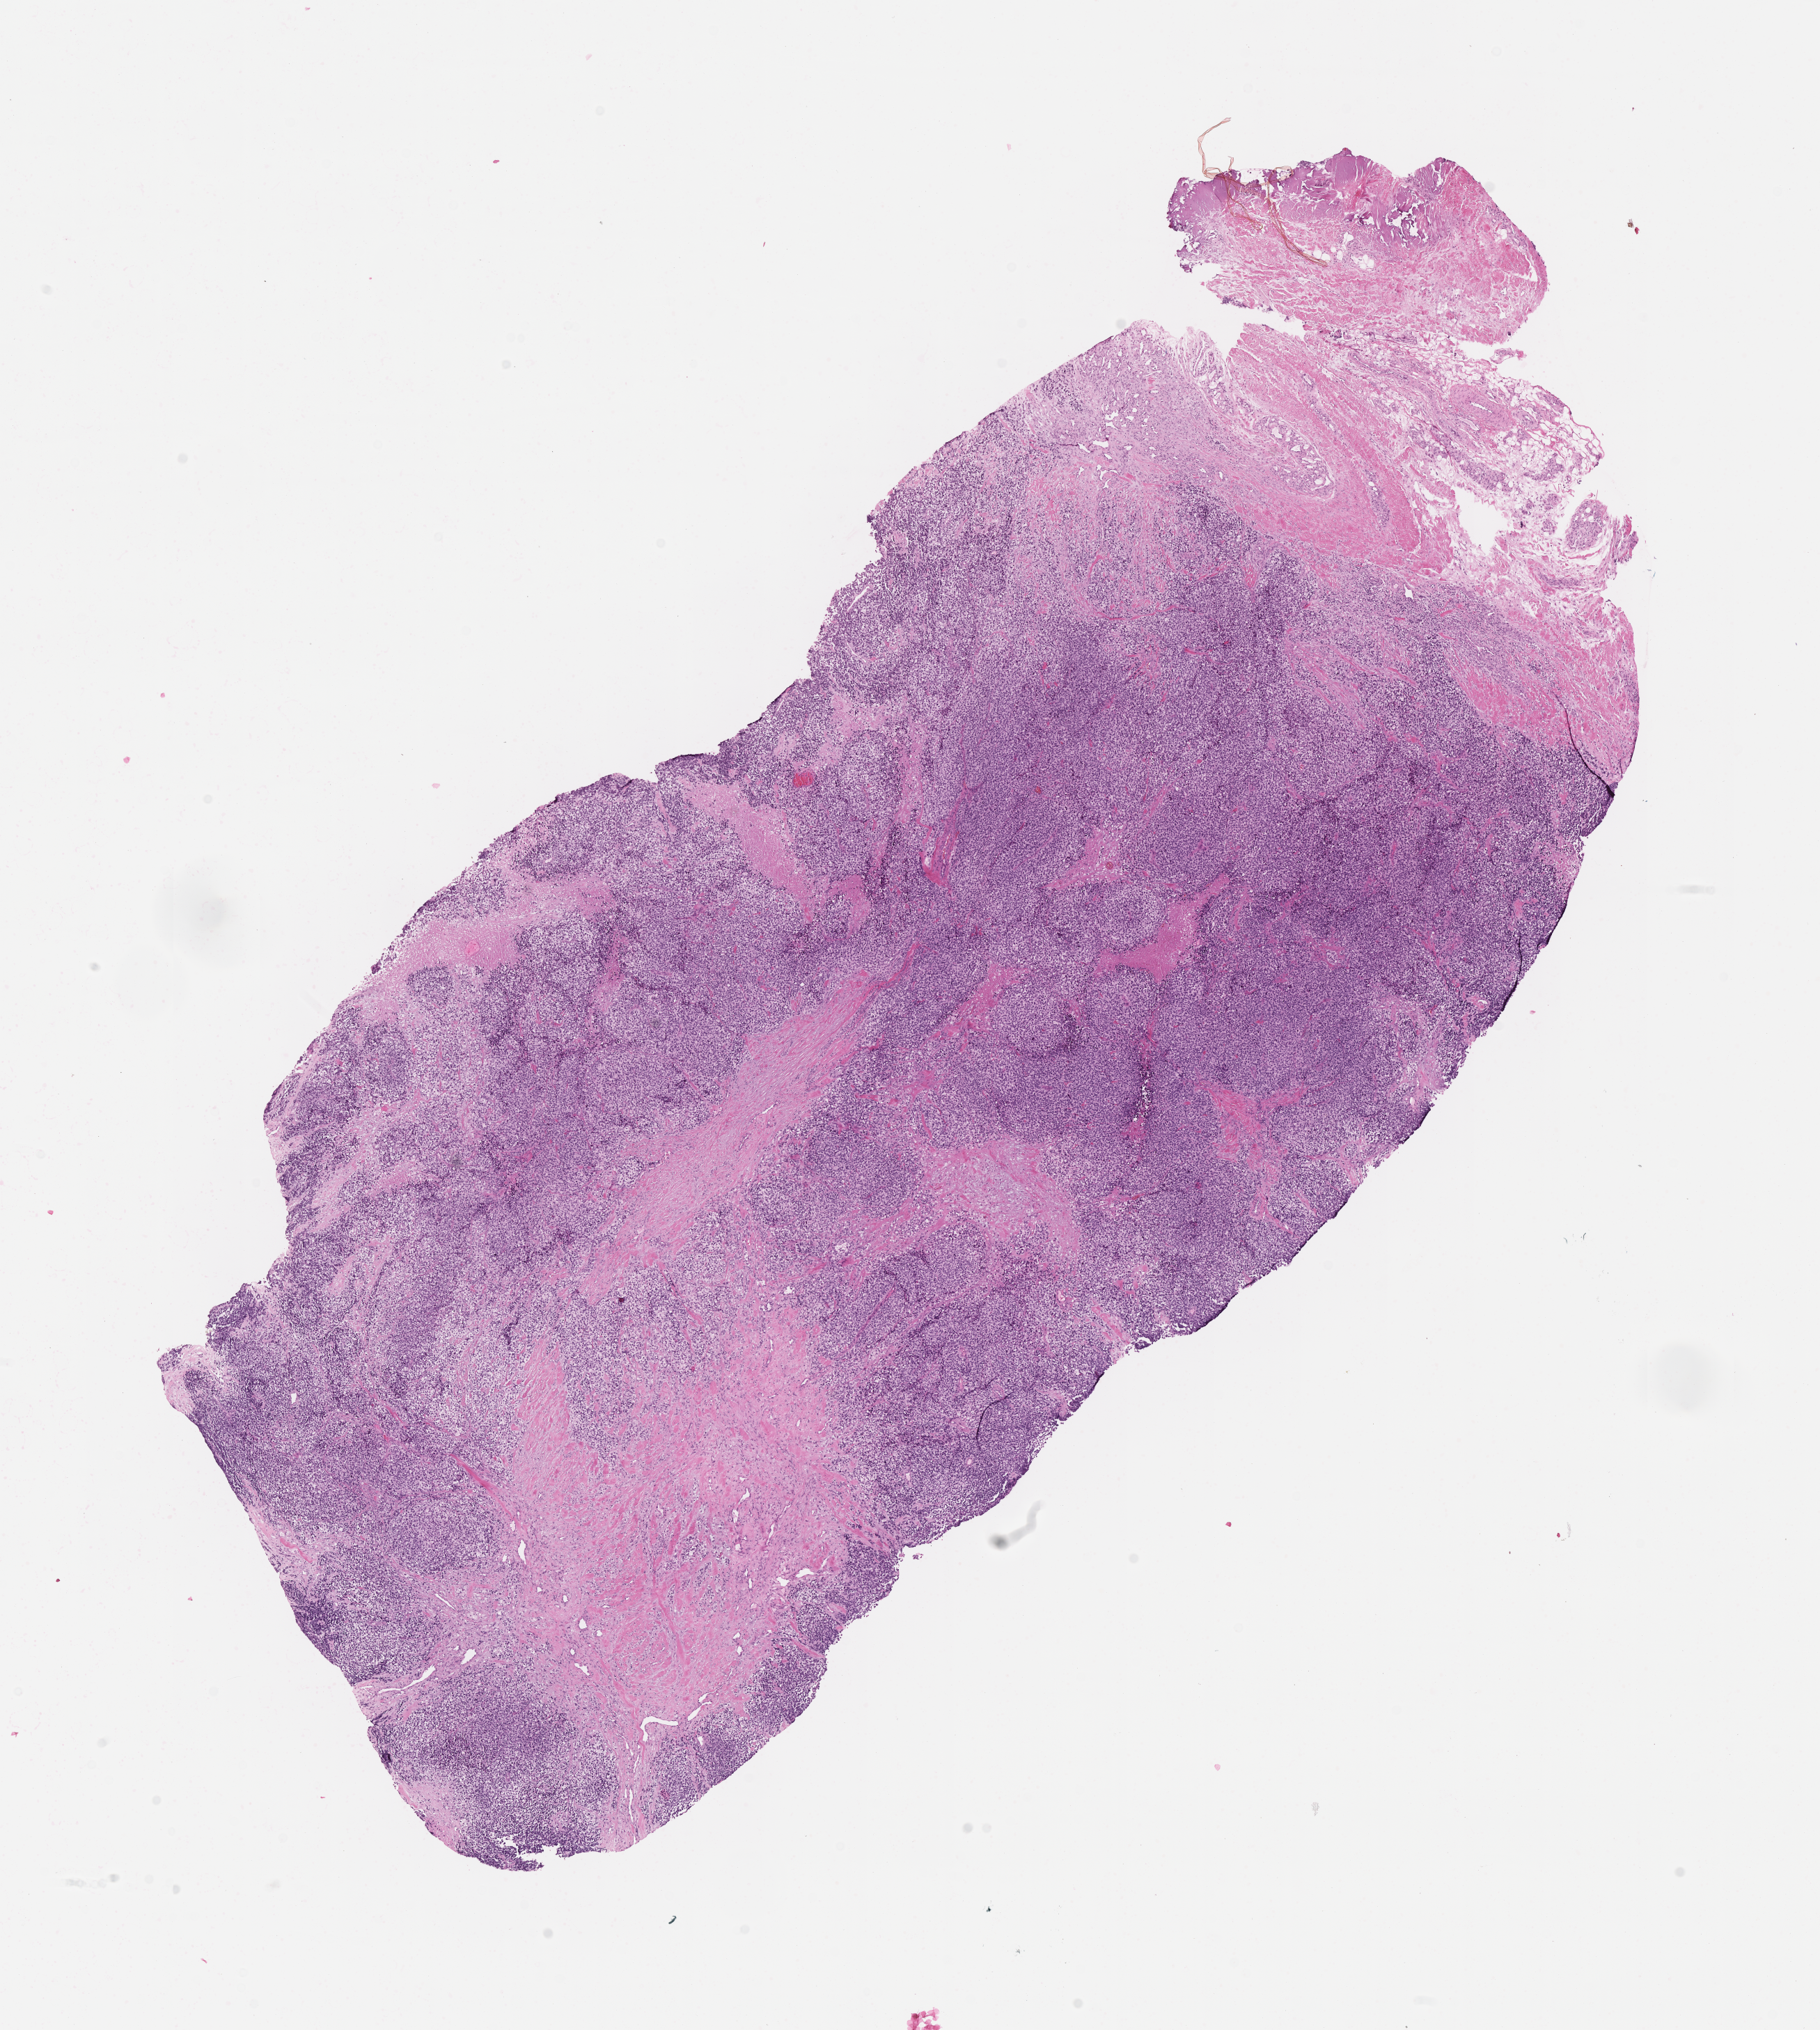
H&E whole-slide image of tumor tissue, whole scanned area (about 10.6 x 11.8 mm) shown as a low-resolution overview, formalin-fixed, paraffin-embedded (FFPE) tissue, site: soft tissue, calf-left. Patient: female, age 10.7 years at diagnosis.
• diagnosis: rhabdomyosarcoma; histological classification: alveolar rhabdomyosarcoma
• metastatic status at presentation (as recorded): metastatic (confirmed)
• stage (as recorded): 4